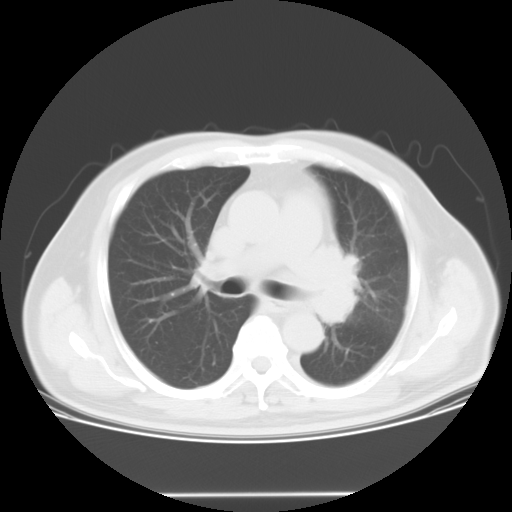
Chest CT, one axial slice. Reconstruction kernel STANDARD. 120 kVp. Lung window (W 1500 / L -600 HU). 512 × 512 image matrix. Male patient, age 61 years. From the clinical record (not read from this slice): clinical TNM (as recorded): T3 N1 M1; histopathological grade: G3.
Structures marked on this image (bounding box drawn by a radiologist):
- lung tumour (recorded histology: small cell carcinoma): bounding box [x1, y1, x2, y2] px = [321, 240, 378, 339]